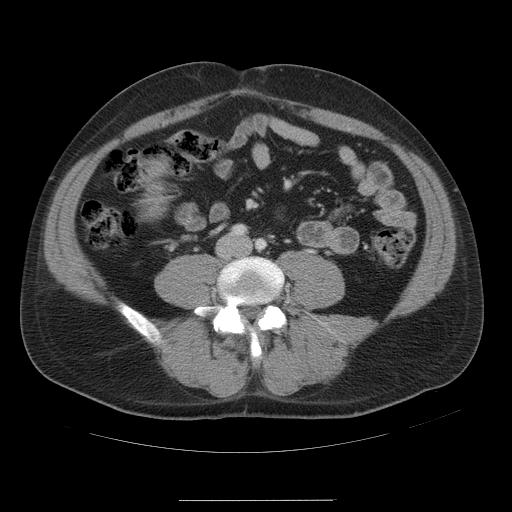
Contrast-enhanced abdominal CT, one axial slice; position 3 of 54 along the scan axis; soft-tissue window (W 400 / L 40 HU); 5 mm slice thickness; 512 × 512 image matrix. Male patient, age 40 years. From the clinical record (not read from this slice): diagnosis: colorectal cancer liver metastases, imaged before liver resection; multiple liver metastases: no; largest metastasis: 15 cm; disease in both lobes: no.
Annotated regions visible in this slice (expert manual segmentation):
- liver: bounding box (x1, y1, x2, y2) in pixels: (141, 162, 164, 216)